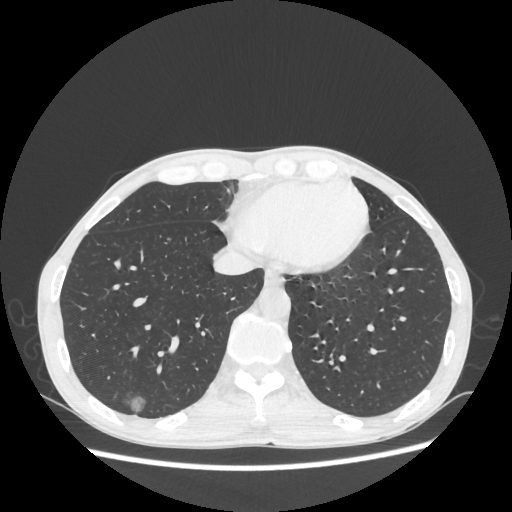
Chest CT, one axial slice; slice 77 of 270 in the series (ordered by position); 100 kVp; lung window (W 1500 / L -600 HU); 1.25 mm slice thickness; 512 × 512 image matrix. Patient: male, 60 years. From the clinical record (not read from this slice): clinical TNM (as recorded): T1c N0 M0.
Outlined on this slice (rectangle marked by the reading radiologist):
- lung tumour (recorded histology: adenocarcinoma): bounding box <118,386,154,418> (left, top, right, bottom; pixels)